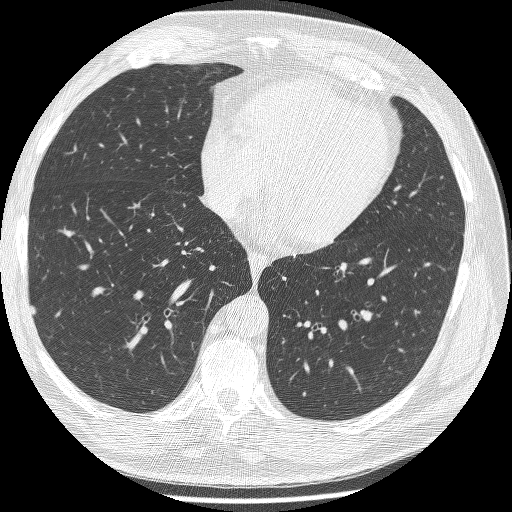
Low-dose screening chest CT, one axial slice; position 92 of 241 along the scan axis; lung window (W 1500 / L -600 HU); 1.25 mm slice thickness; 512 × 512 image matrix, field of view 346 × 346 mm.
Outlined on this slice (outlined manually by an expert reader):
- lesion 2 (tumor, lower lobe of right lung): bounding box <30,305,36,316> (left, top, right, bottom; pixels)